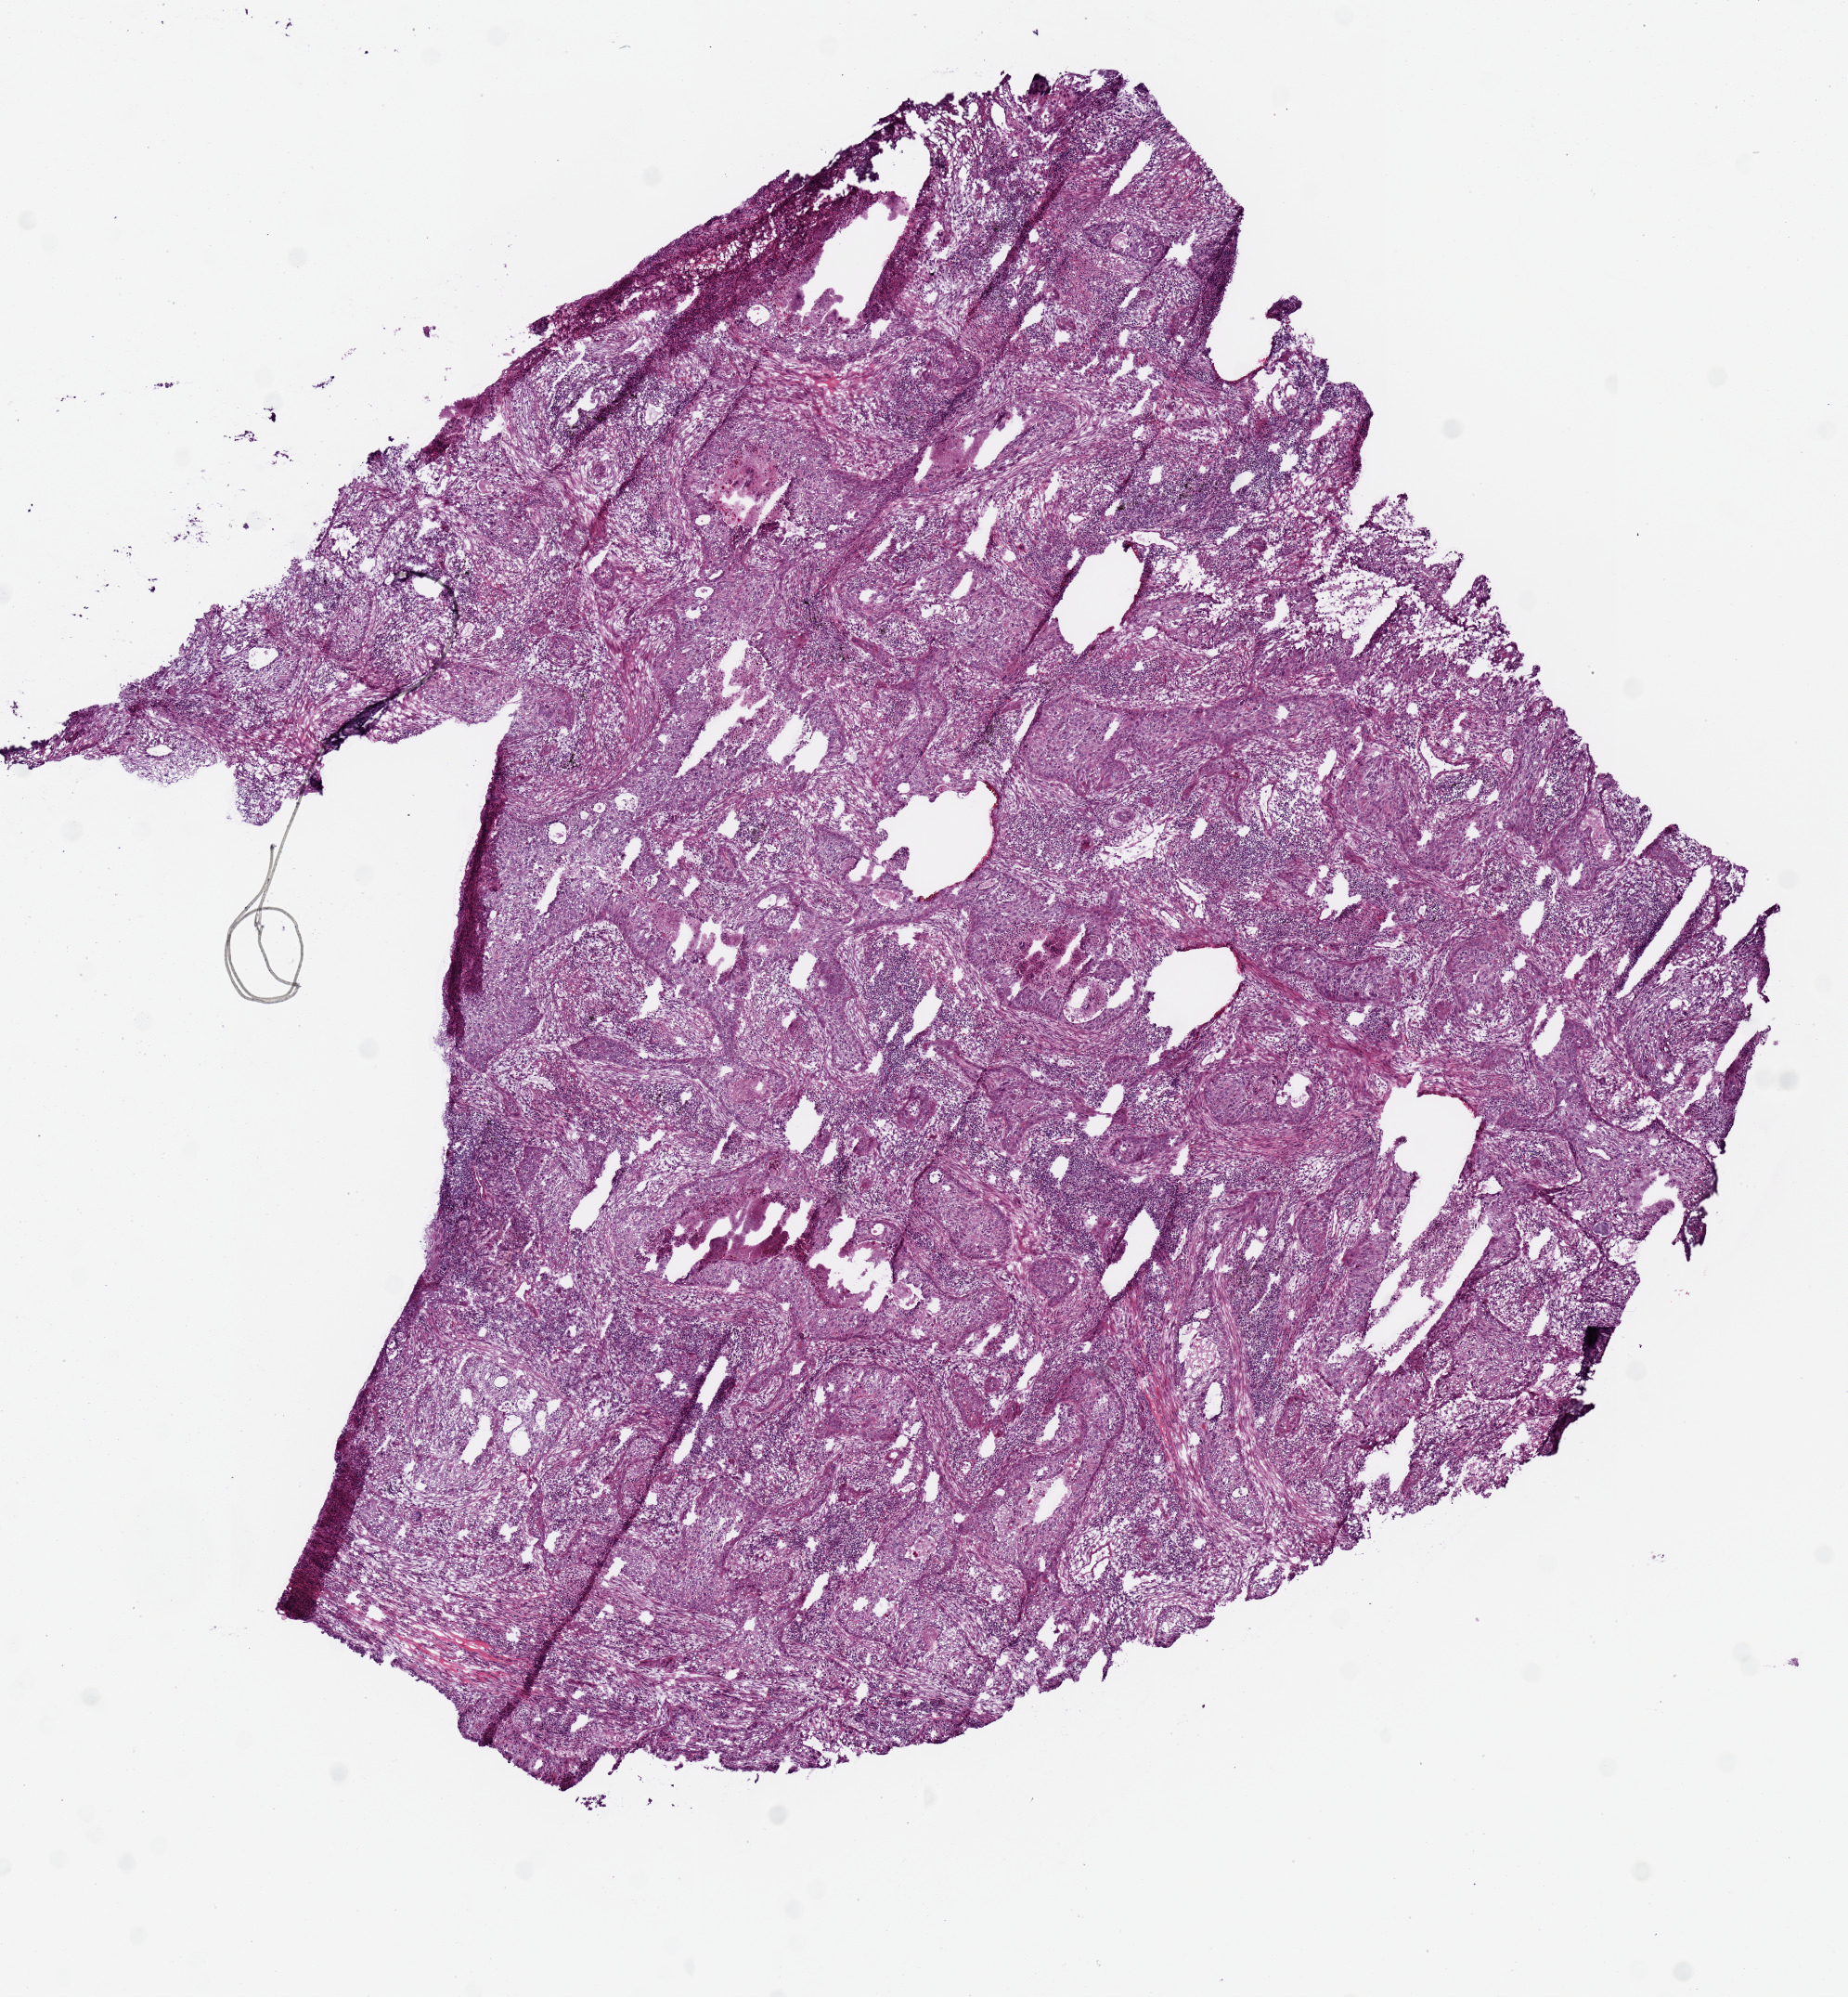
Digitized H&E-stained tissue section (whole slide) — whole scanned area (about 7.9 x 8.5 mm, from a 20x scan) shown as a low-resolution overview. Frozen section from the top of the tissue portion. Primary tumour sample from the lung. Patient: male, age at initial diagnosis 74 years. Composition of this section per pathologist review: tumour cells 77%, tumour nuclei 65%, normal cells 0%, stromal cells 15%, necrosis 8%.
Laterality: left. AJCC pathologic stage: IA (7th edition). Pathologic diagnosis: Squamous cell carcinoma, NOS (upper lobe, lung). TNM: T1b N0 MX.